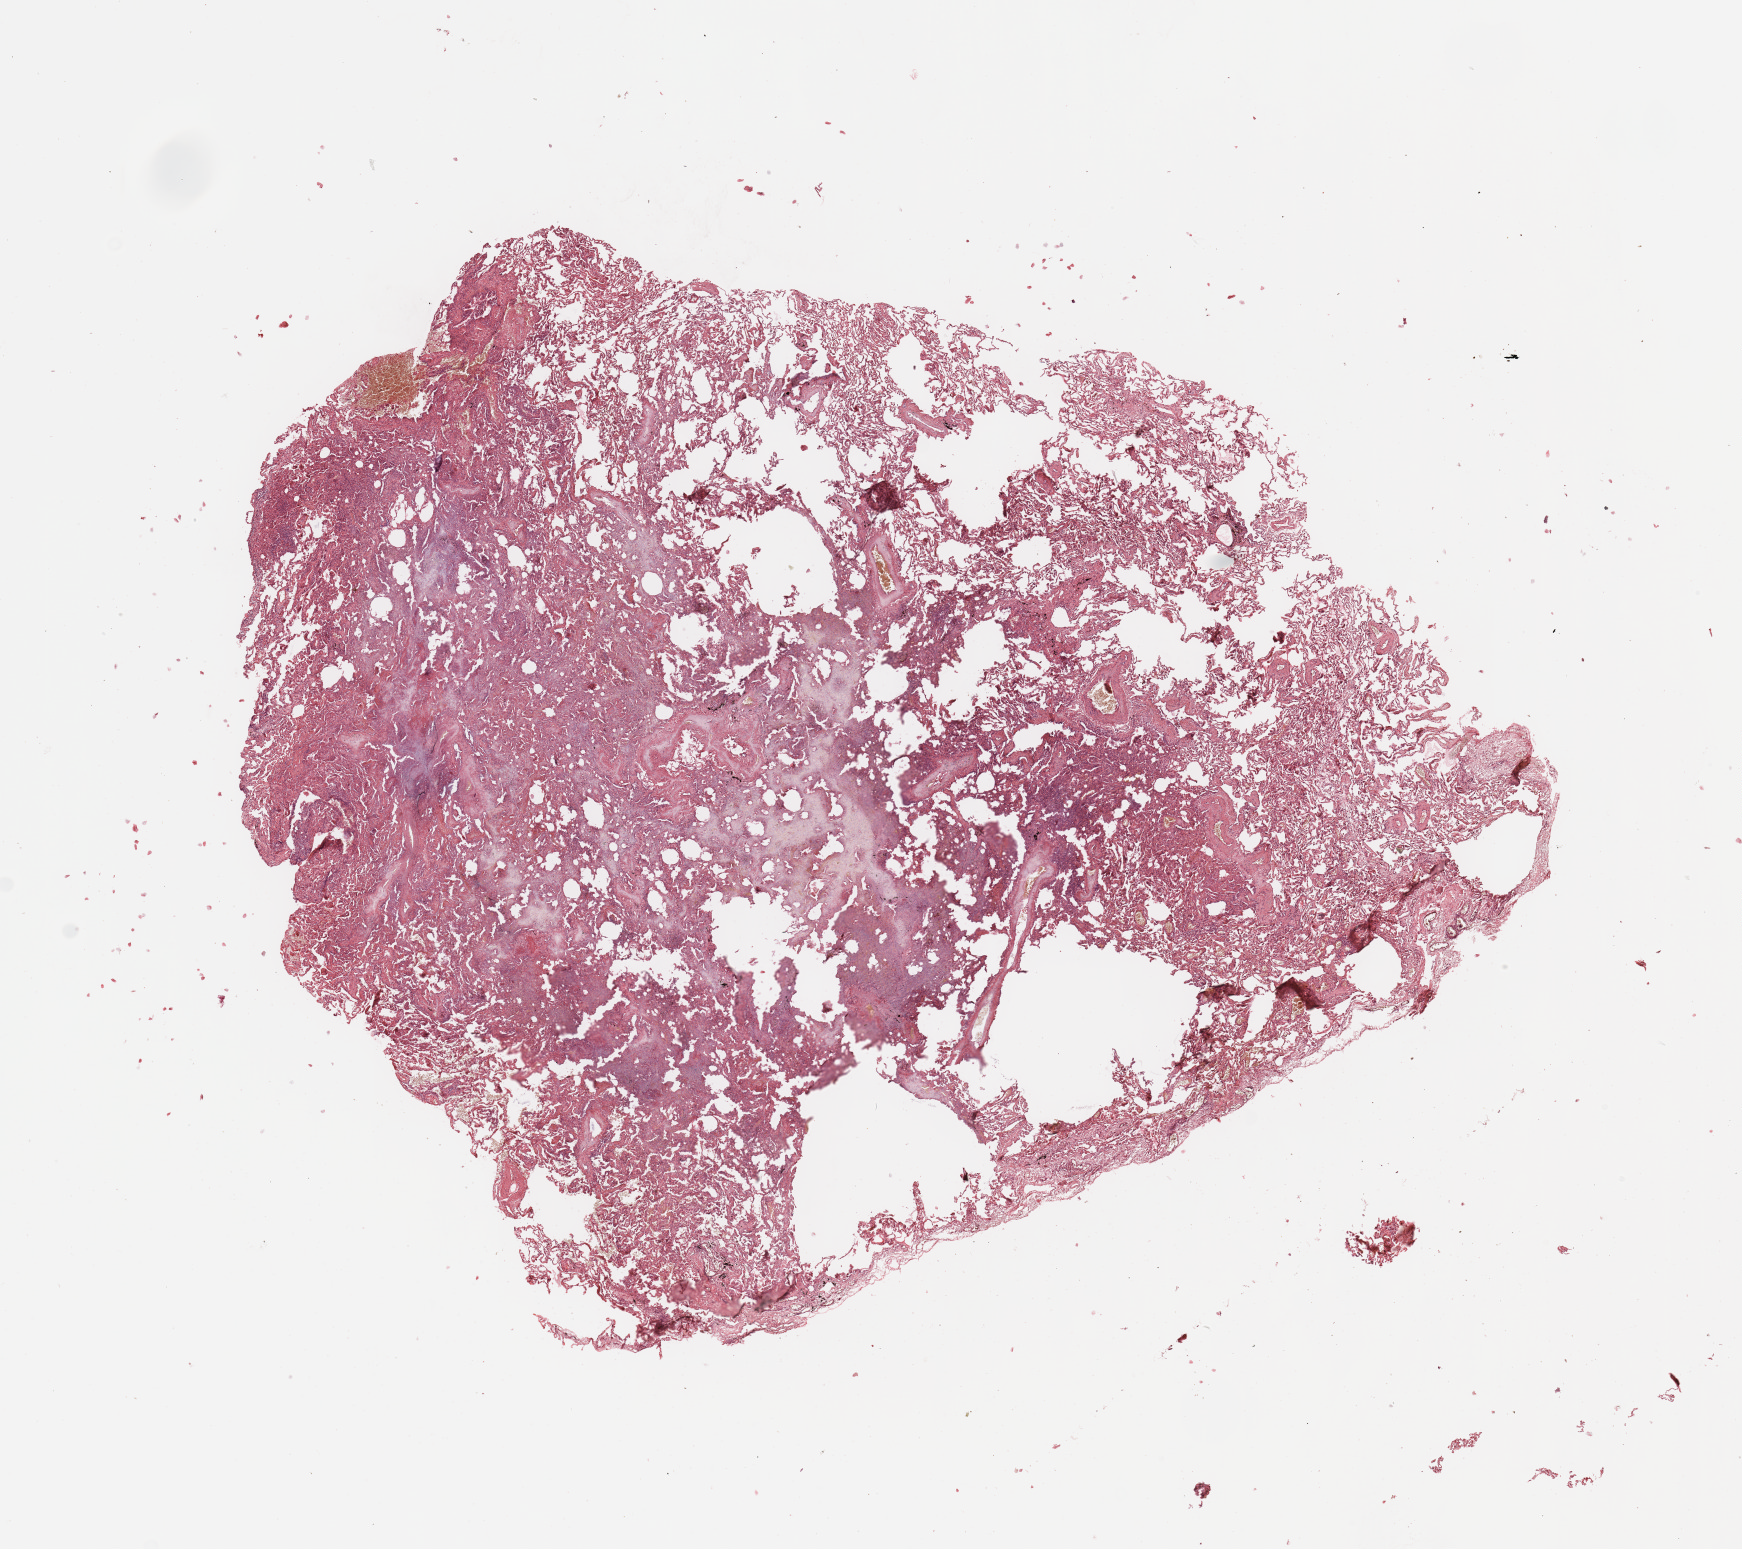
Whole-slide histology image, H&E, a low-resolution overview of the entire scanned area, about 13.8 x 12.3 mm (slide scanned at 20x). Normal (non-tumour) tissue sample, lung. 69-year-old male patient.
This section: normal (non-tumour) tissue from the same patient. Patient diagnosis: Adenocarcinoma, NOS.